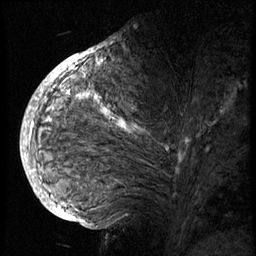
Breast MRI (dynamic contrast-enhanced), one sagittal slice. 3 images stored at this slice position (order not interpretable as contrast timing). 1.5 T. TE 4.2 ms, TR 8.9 ms. 2.5 mm slice thickness. 256 × 256 image matrix. Patient: female, 57 years. Case-level facts recorded for this patient, not image findings: setting: breast cancer imaged before/during neoadjuvant chemotherapy; receptor status: HER2-positive.
Structures marked on this image (semi-automatic segmentation, software-assisted and operator-edited):
- analysis volume of interest (the breast-tissue region the enhancement analysis was run in; not a lesion): bounding box <40,62,240,175> (left, top, right, bottom; pixels)
- tumour enhancement mask (voxels above the 140 % enhancement threshold inside the analysis volume of interest): <51,62,183,157>